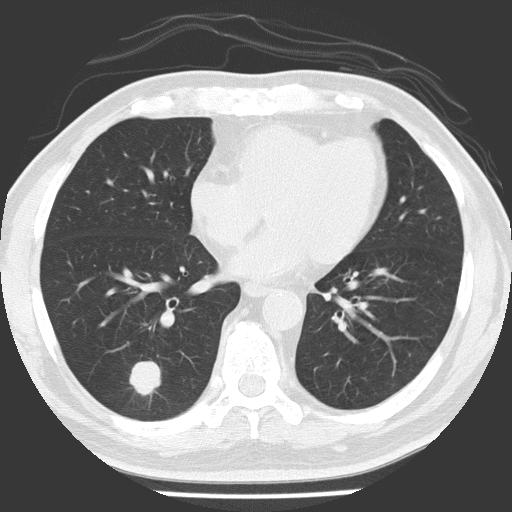
Low-dose screening chest CT, one axial slice; position 65 of 154 along the scan axis; 120 kVp; lung window (W 1500 / L -600 HU); 2 mm slice thickness; 512 × 512 image matrix.
Structures marked on this image (manually delineated by an expert):
- lesion 1 (tumor, lower lobe of right lung): bounding box <129,361,161,396> (left, top, right, bottom; pixels)